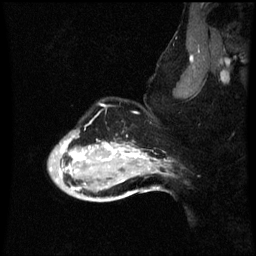
Breast MRI (dynamic contrast-enhanced), one sagittal slice; position 48 of 60 along the scan axis; dynamic contrast-enhanced series, image 2 of 3 at this slice position (ordered by acquisition); 1.5 T; TE 4.2 ms, TR 8.9 ms; 256 × 256 image matrix. Female patient, age 49 years. Case-level facts recorded for this patient, not image findings: setting: breast cancer imaged before/during neoadjuvant chemotherapy; receptor status: HR-positive, HER2-negative.
Annotated regions visible in this slice (semi-automatically segmented with operator editing):
- analysis volume of interest (the breast-tissue region the enhancement analysis was run in; not a lesion): bounding box (x1, y1, x2, y2) in pixels: (48, 128, 159, 199)
- tumour enhancement mask (voxels above the 70 % enhancement threshold inside the analysis volume of interest): (60, 140, 145, 191)